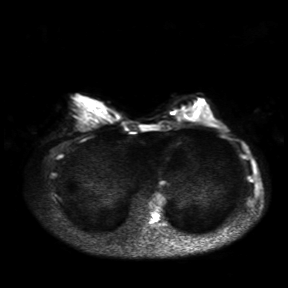
Breast MRI, one axial slice. Position 12 of 30 along the scan axis. Diffusion-weighted series; image 2 of 4 stored at this slice position (different b-values; order by instance number). 3 T. 4 mm slice thickness. 288 × 288 image matrix, field of view 360 × 360 mm. Female patient.
Annotated regions visible in this slice (manually delineated by an expert):
- tumour on diffusion-weighted imaging: bounding box <173,109,185,117> (left, top, right, bottom; pixels)